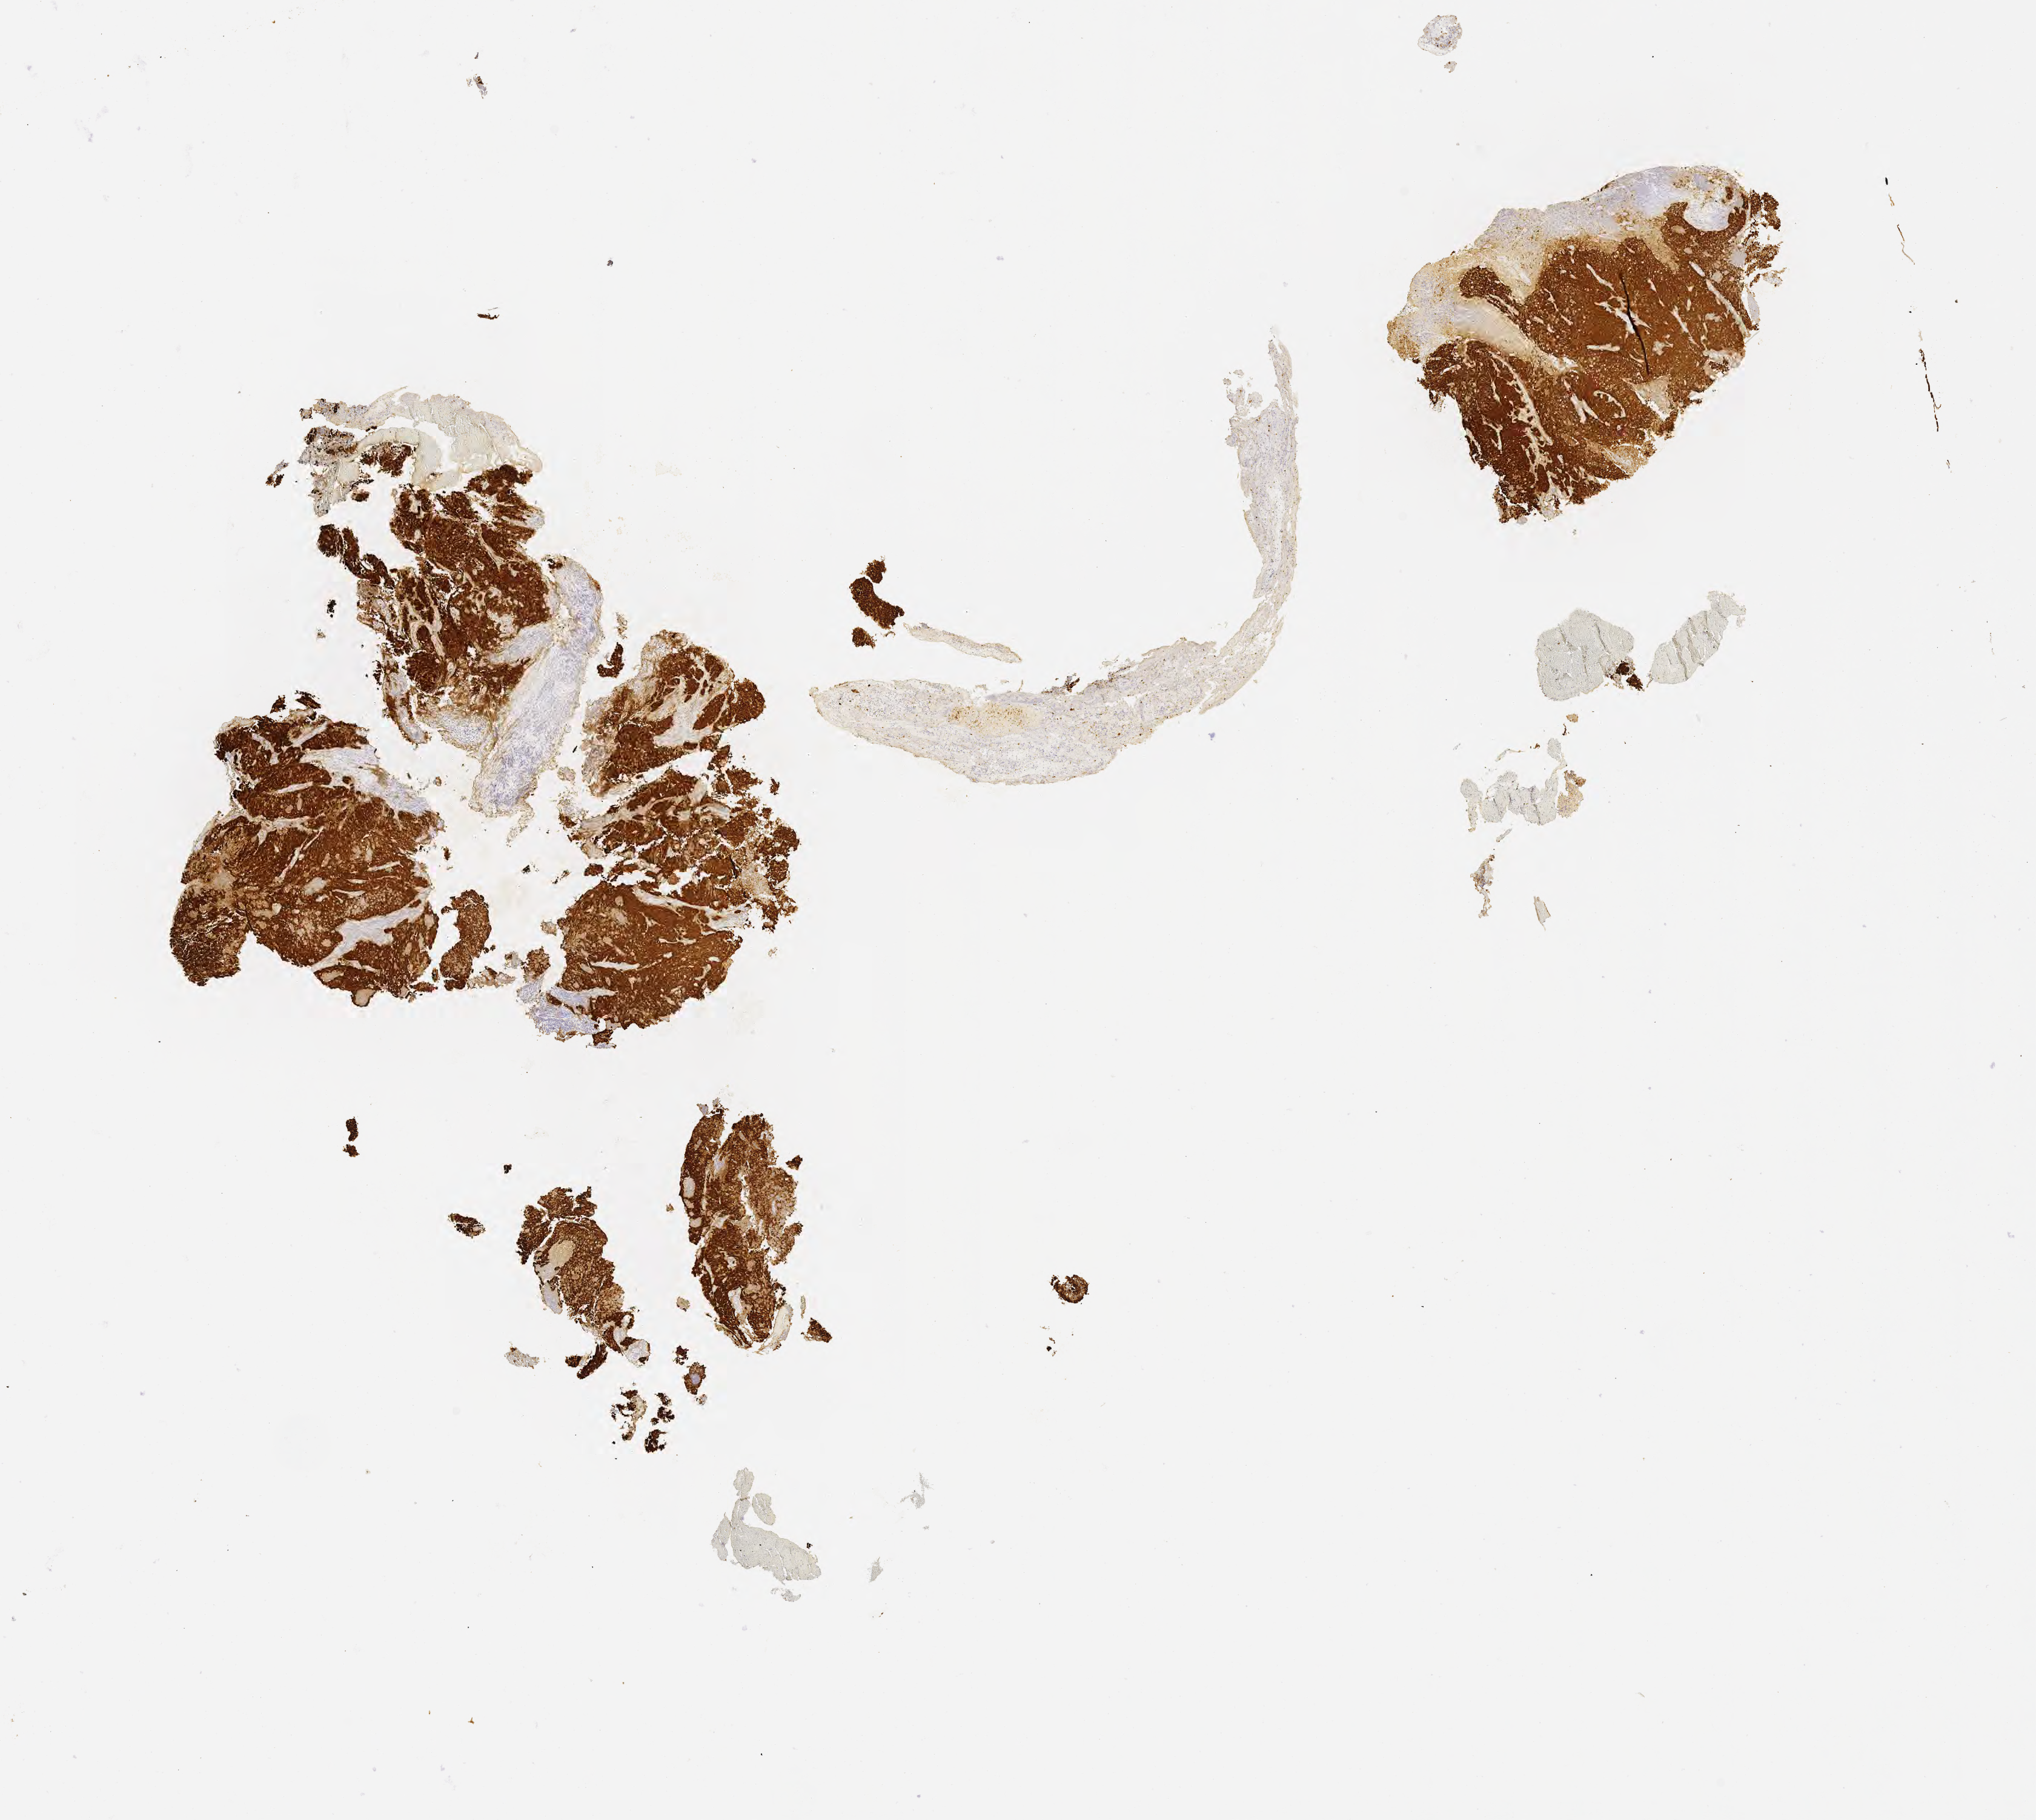
IHC for p16 (p16INK4a), whole-slide image — shown as a low-resolution overview of the whole scanned area (about 13.6 x 12.1 mm); specimen: tumor tissue; anatomic site: cervix. Patient female; age 33 years.
Histologic diagnosis: Squamous cell carcinoma, large cell, nonkeratinizing, NOS.